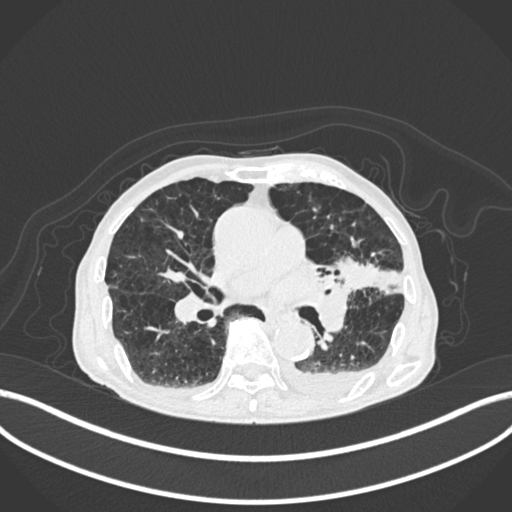
Chest CT, one axial slice. Slice 115 of 400 in the series (ordered by position). Reconstruction kernel B30f. 120 kVp. Lung window (W 1500 / L -600 HU). 512 × 512 image matrix, field of view 400 × 400 mm. Patient: male, 90 years or older. Case-level facts recorded for this patient, not image findings: clinical TNM (as recorded): T2b N1 M0.
Annotated regions visible in this slice (bounding box drawn by a radiologist):
- lung tumour (recorded histology: squamous cell carcinoma): bounding box <325,243,390,292> (left, top, right, bottom; pixels)